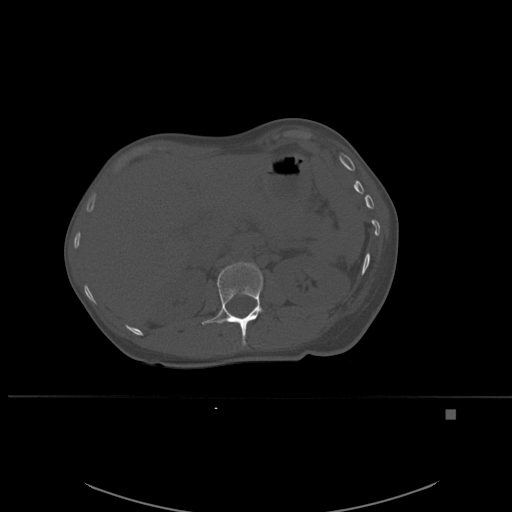
CT including the spine, one axial slice. Slice 259 of 537 in the series (ordered by position). Bone window (W 1800 / L 400 HU). 1.5 mm slice thickness. 512 × 512 image matrix. Female patient, age 45 years. Case-level facts recorded for this patient, not image findings: primary cancer: lung.
Outlined on this slice (semi-automatically segmented with operator editing):
- L1 vertebra: bounding box [x1, y1, x2, y2] px = [201, 262, 264, 346]